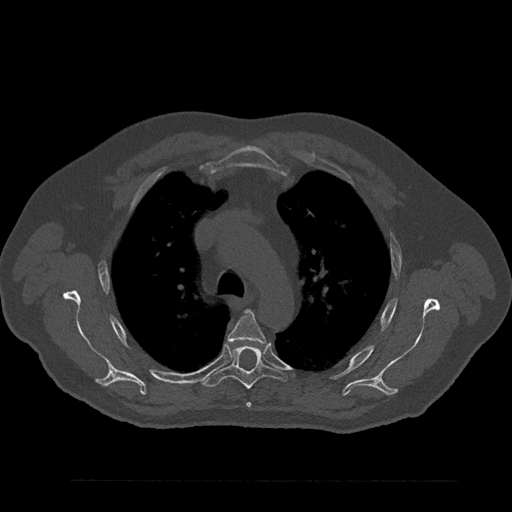
CT including the spine, one axial slice; slice 616 of 797 in the series (ordered by position); bone window (W 1800 / L 400 HU); 0.5 mm slice thickness; 512 × 512 image matrix, field of view 430 × 430 mm. Patient: male, 61 years. From the clinical record (not read from this slice): primary cancer: prostate.
Structures marked on this image (semi-automatic segmentation, software-assisted and operator-edited):
- T4 vertebra: bounding box <227,310,266,408> (left, top, right, bottom; pixels)
- T5 vertebra: <202,346,288,389>